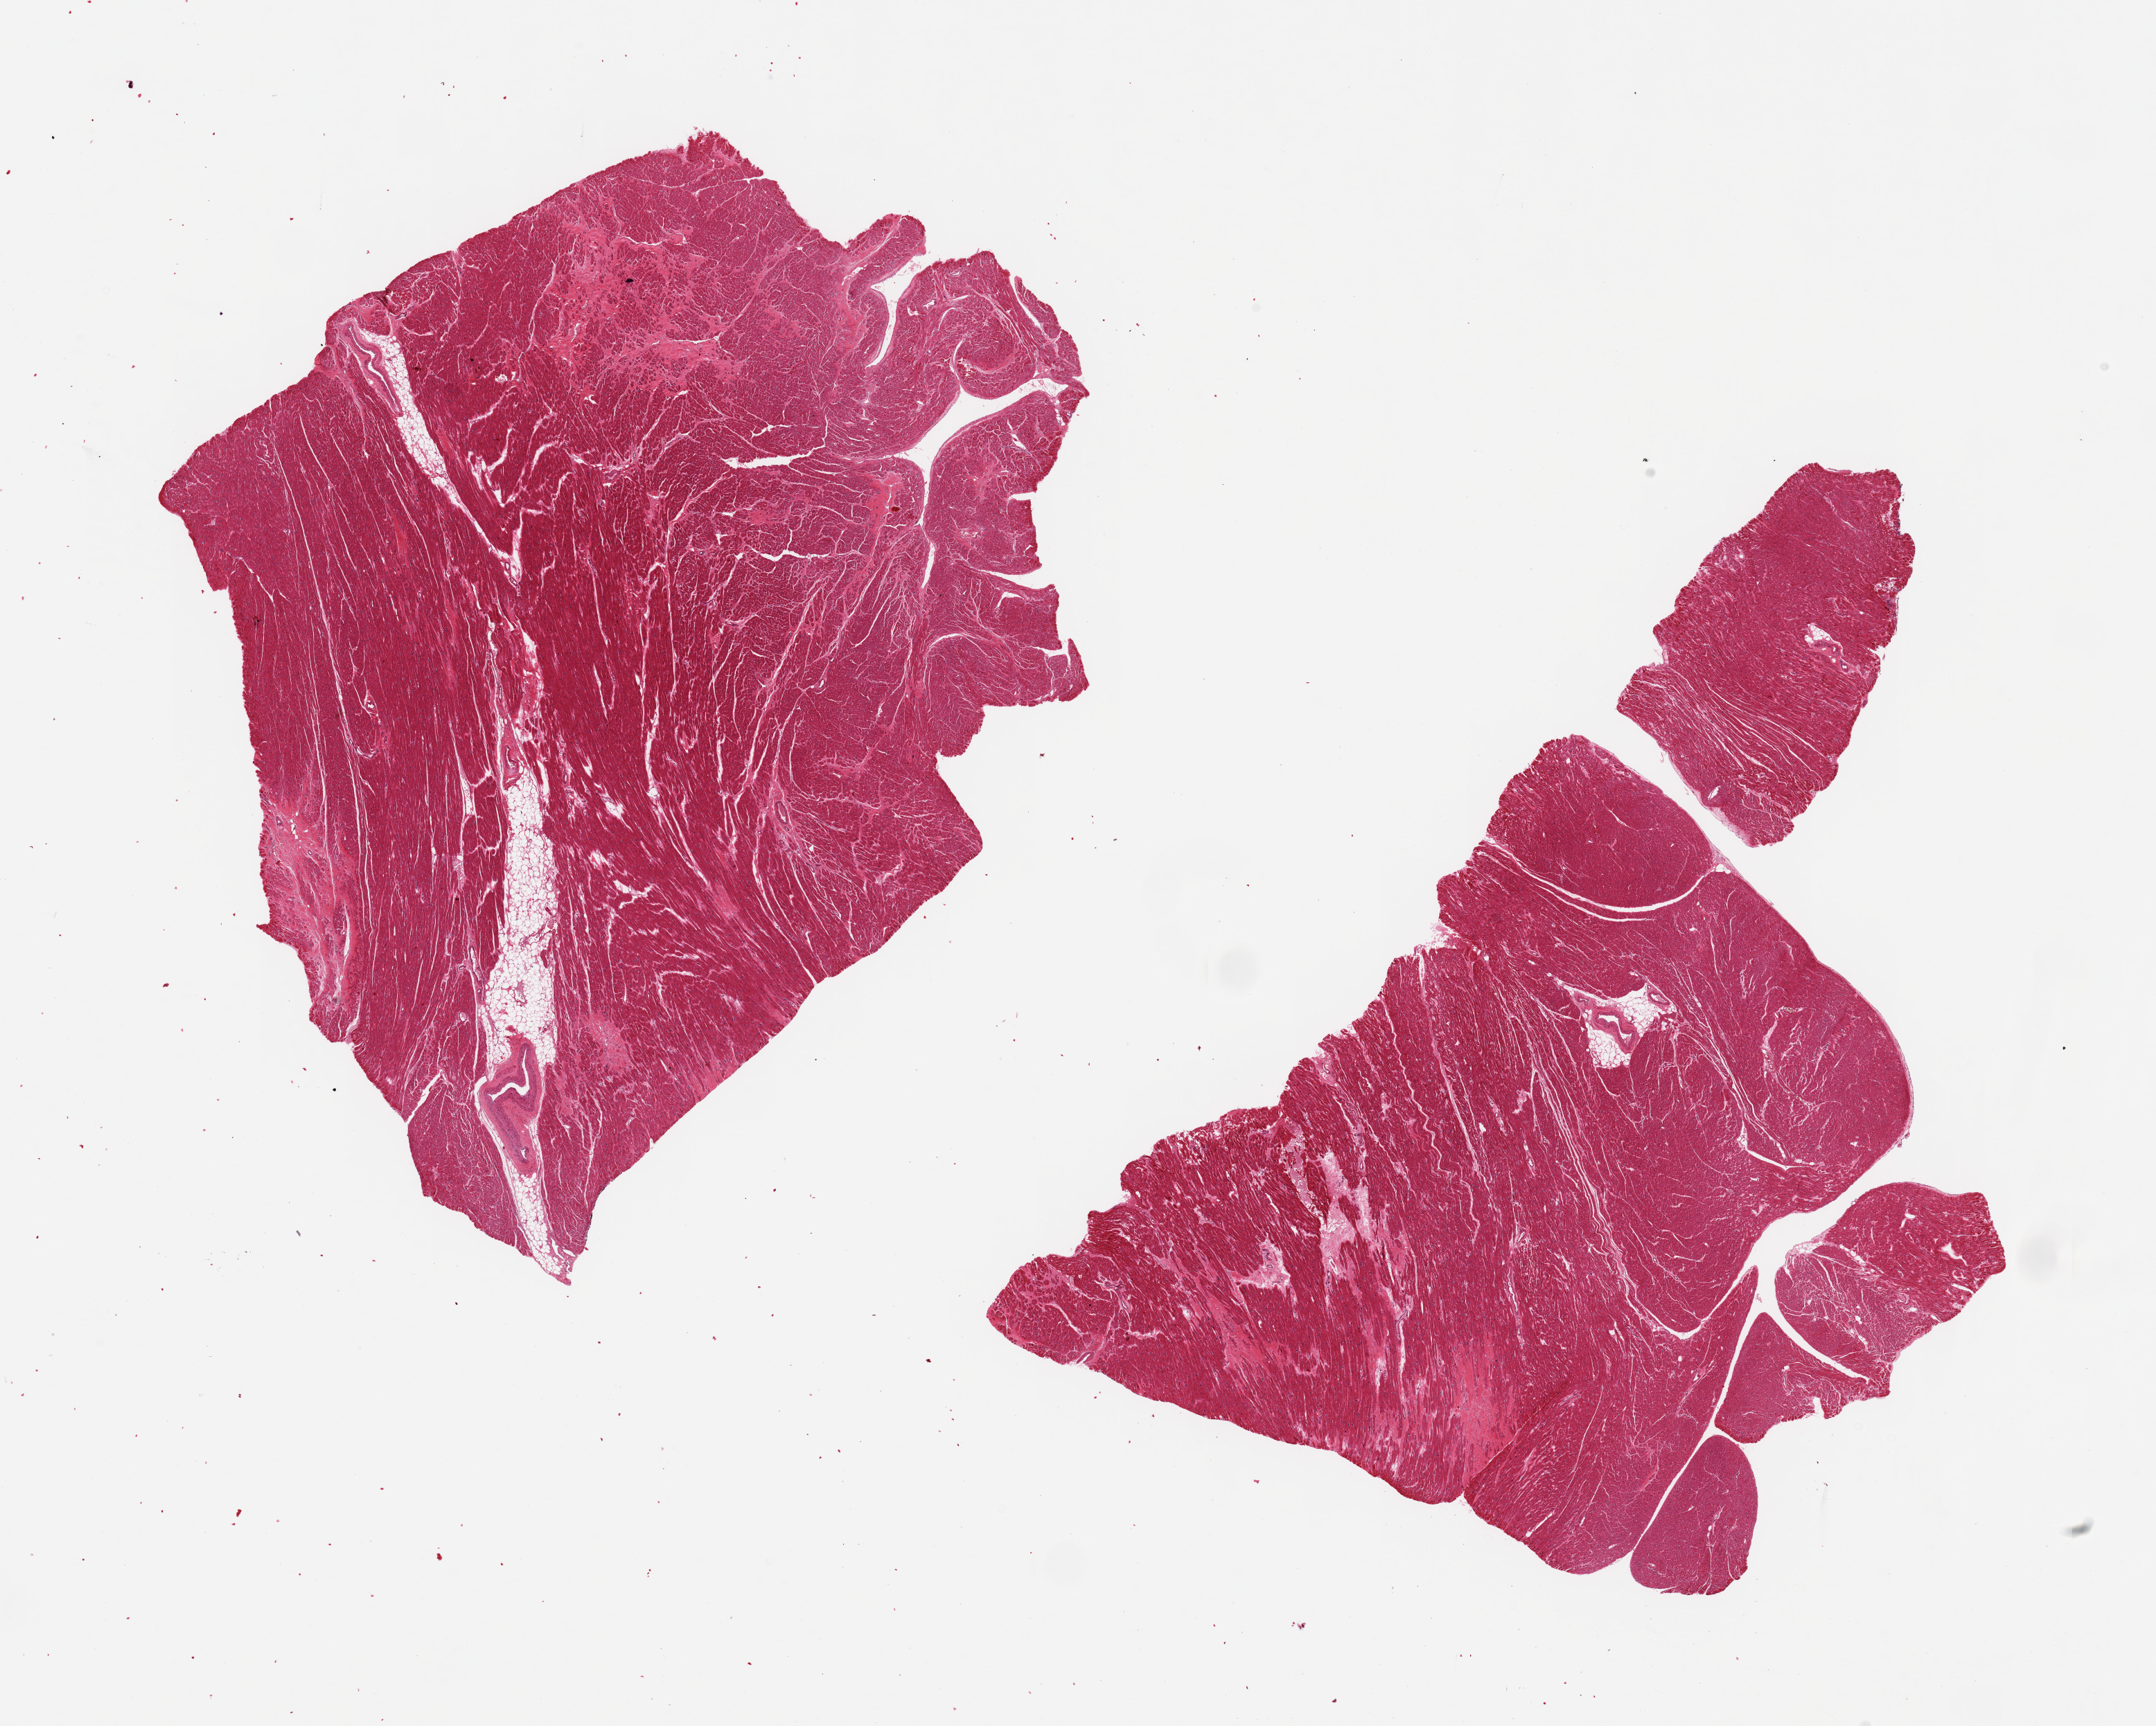
Whole-slide image, haematoxylin and eosin stain, brightfield, shown as a low-resolution overview of the whole scanned area (about 24.6 x 19.7 mm). PAXgene-fixed paraffin-embedded (PFPE) section. Section of heart (target tissue). Tissue donor sample. Male donor.
Review note (as recorded): 2 pieces, patchy fibrotic infarcts present in both.